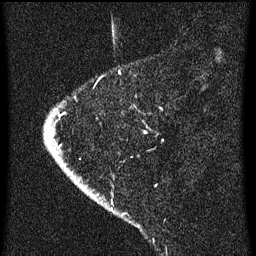
Breast MRI (dynamic contrast-enhanced), one sagittal slice; slice 11 of 60 in the series (ordered by position); dynamic contrast-enhanced series, image 2 of 3 at this slice position (ordered by acquisition); 1.5 T; TE 4.2 ms, TR 8 ms; 2 mm slice thickness; 256 × 256 image matrix, field of view 180 × 180 mm. Patient: female, 47 years.
Structures marked on this image (semi-automatic segmentation, software-assisted and operator-edited):
- analysis volume of interest (the breast-tissue region the enhancement analysis was run in; not a lesion): bounding box <43,76,160,193> (left, top, right, bottom; pixels)
- tumour enhancement mask (voxels above the 70 % enhancement threshold inside the analysis volume of interest): <47,126,60,149>